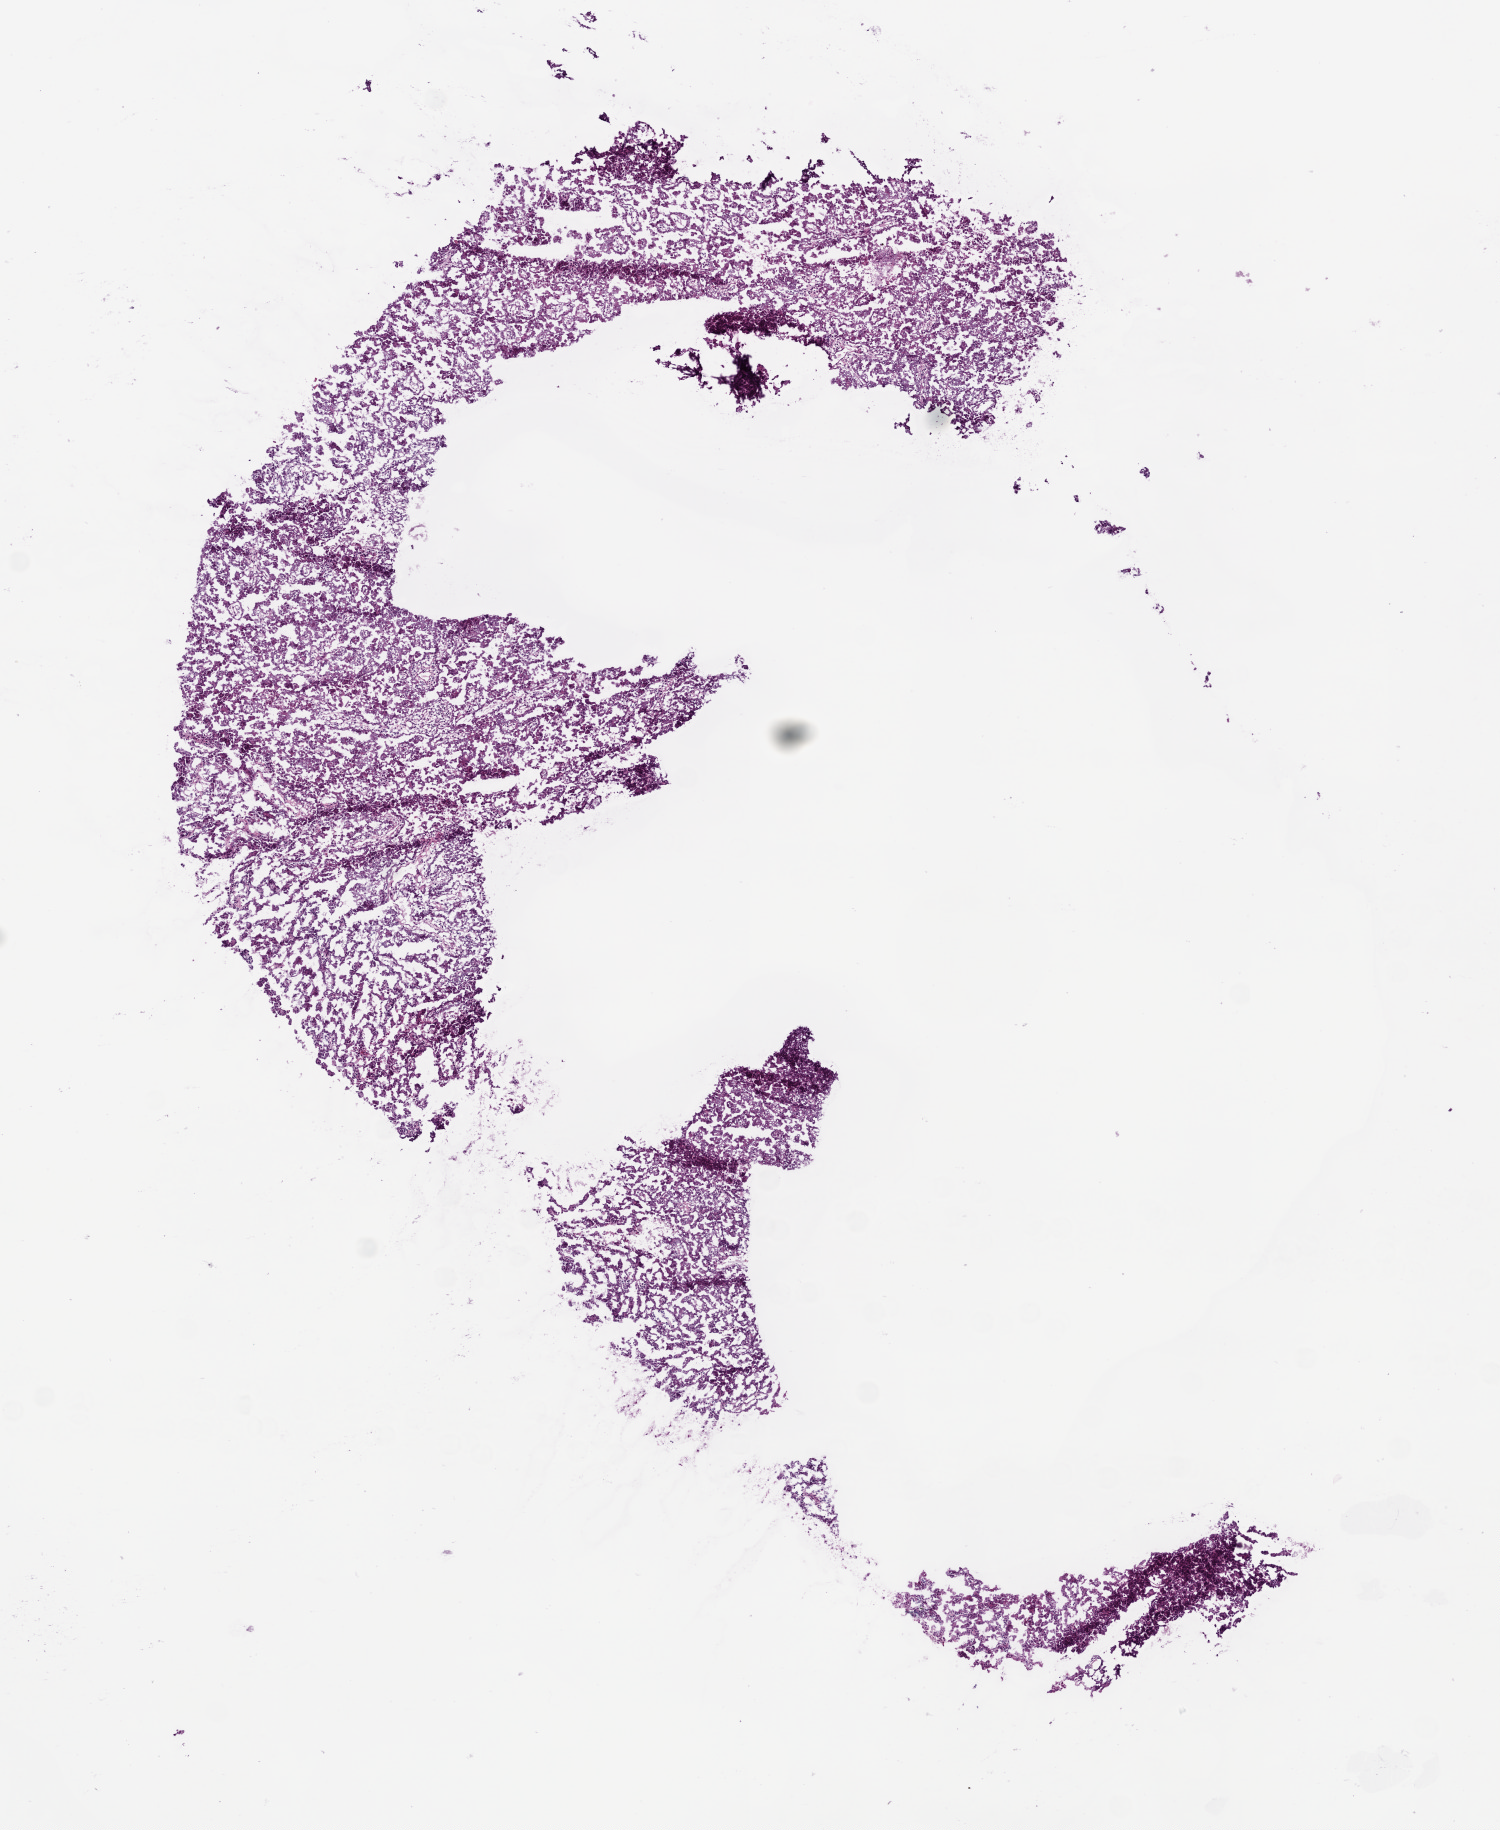
Whole-slide histology image, H&E, low-resolution overview of the scanned area, about 6.0 x 7.3 mm; frozen section from the bottom of the tissue portion; sample: primary tumour, kidney. Female patient; age at initial diagnosis 75 years. Pathologist review of this section (percent, as recorded): tumour cells 78%, tumour nuclei 85%, normal cells 0%, stromal cells 20%, necrosis 2%.
* pathologic diagnosis: Papillary adenocarcinoma, NOS